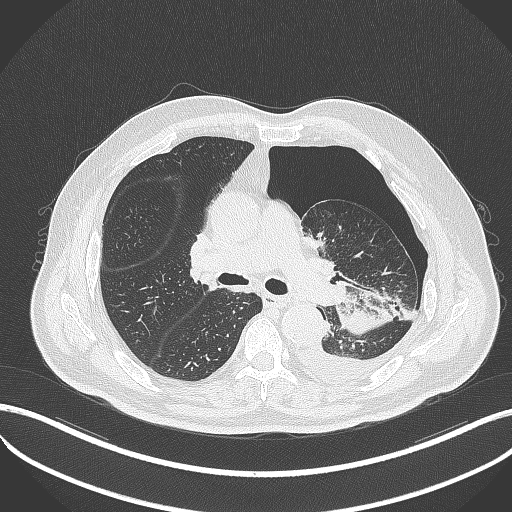
Chest CT, one axial slice; slice 314 of 464 in the series (ordered by position); lung window (W 1500 / L -600 HU); 1 mm slice thickness; 512 × 512 image matrix, field of view 400 × 400 mm. Patient: male, 76 years. From the clinical record (not read from this slice): clinical TNM (as recorded): T3 N0 M1b.
Structures marked on this image (rectangle marked by the reading radiologist):
- lung tumour (recorded histology: adenocarcinoma): box from (x=337, y=291) to (x=394, y=335) px